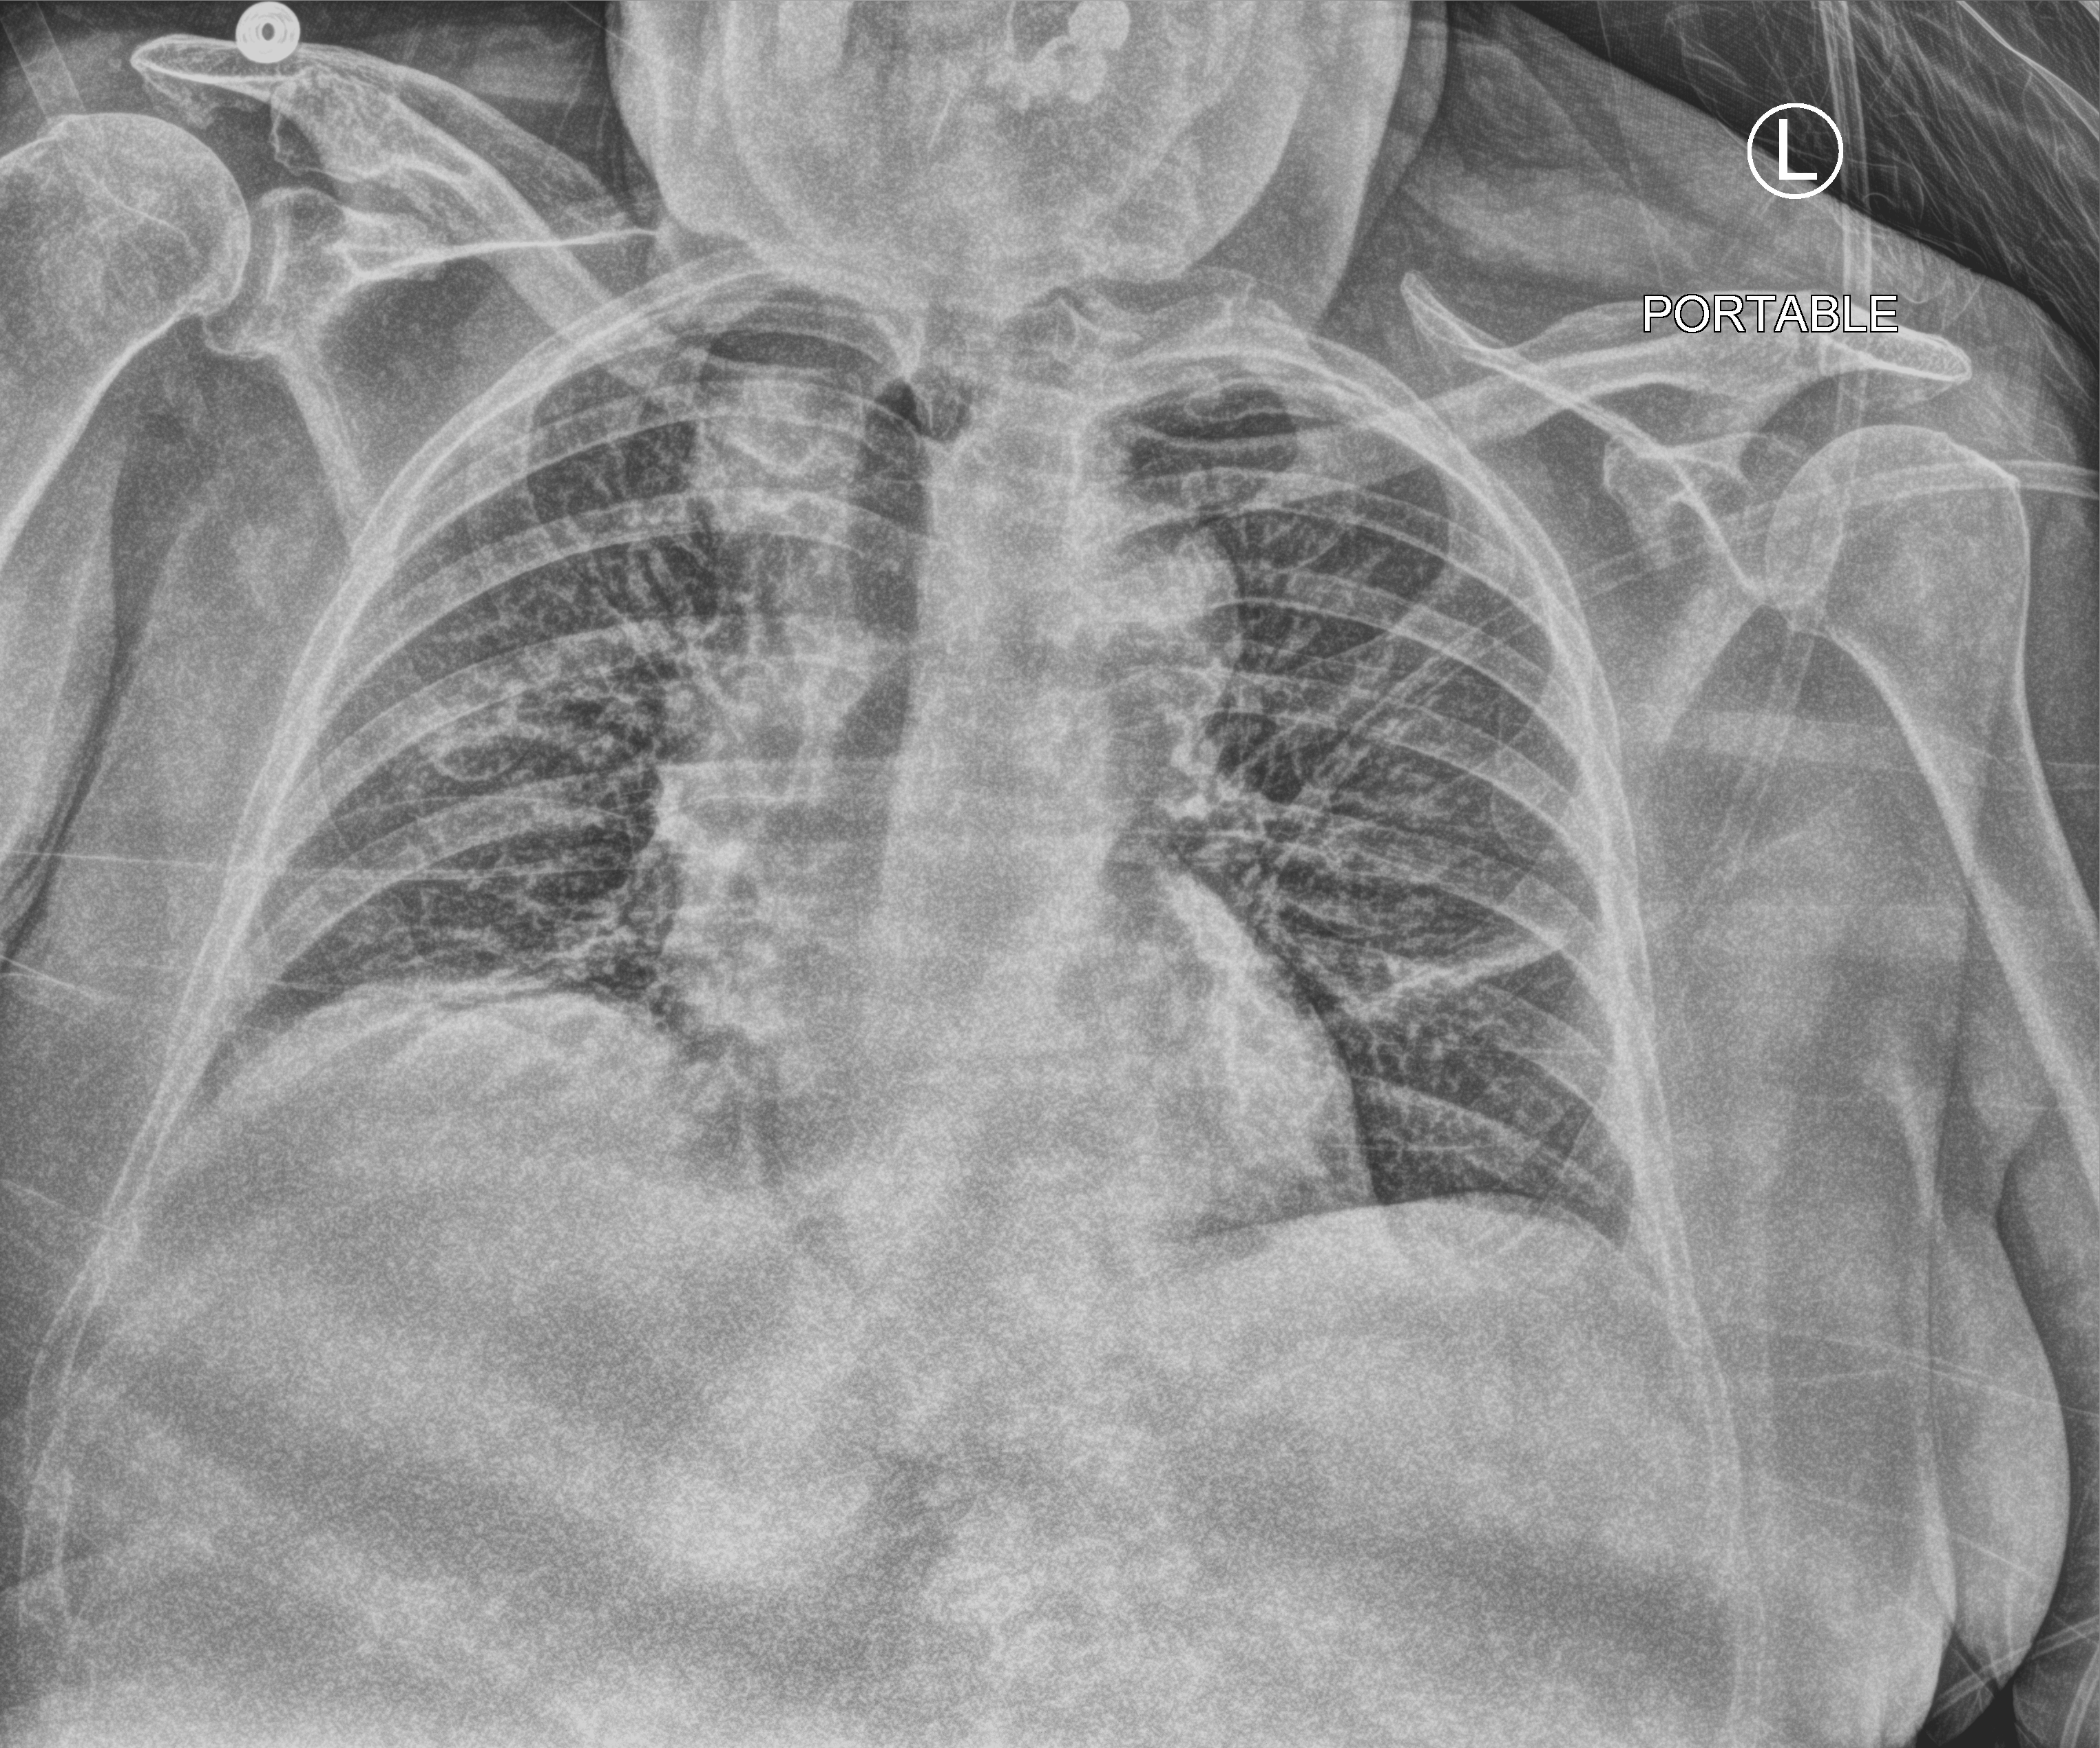
Bedside chest radiograph (computed radiography); anteroposterior (AP) projection. Female patient hospitalised with COVID-19, age 75–90 years.
Admission-level facts for this patient (not findings on this image; timing relative to this image not recorded): mechanically ventilated during this hospital stay: no.